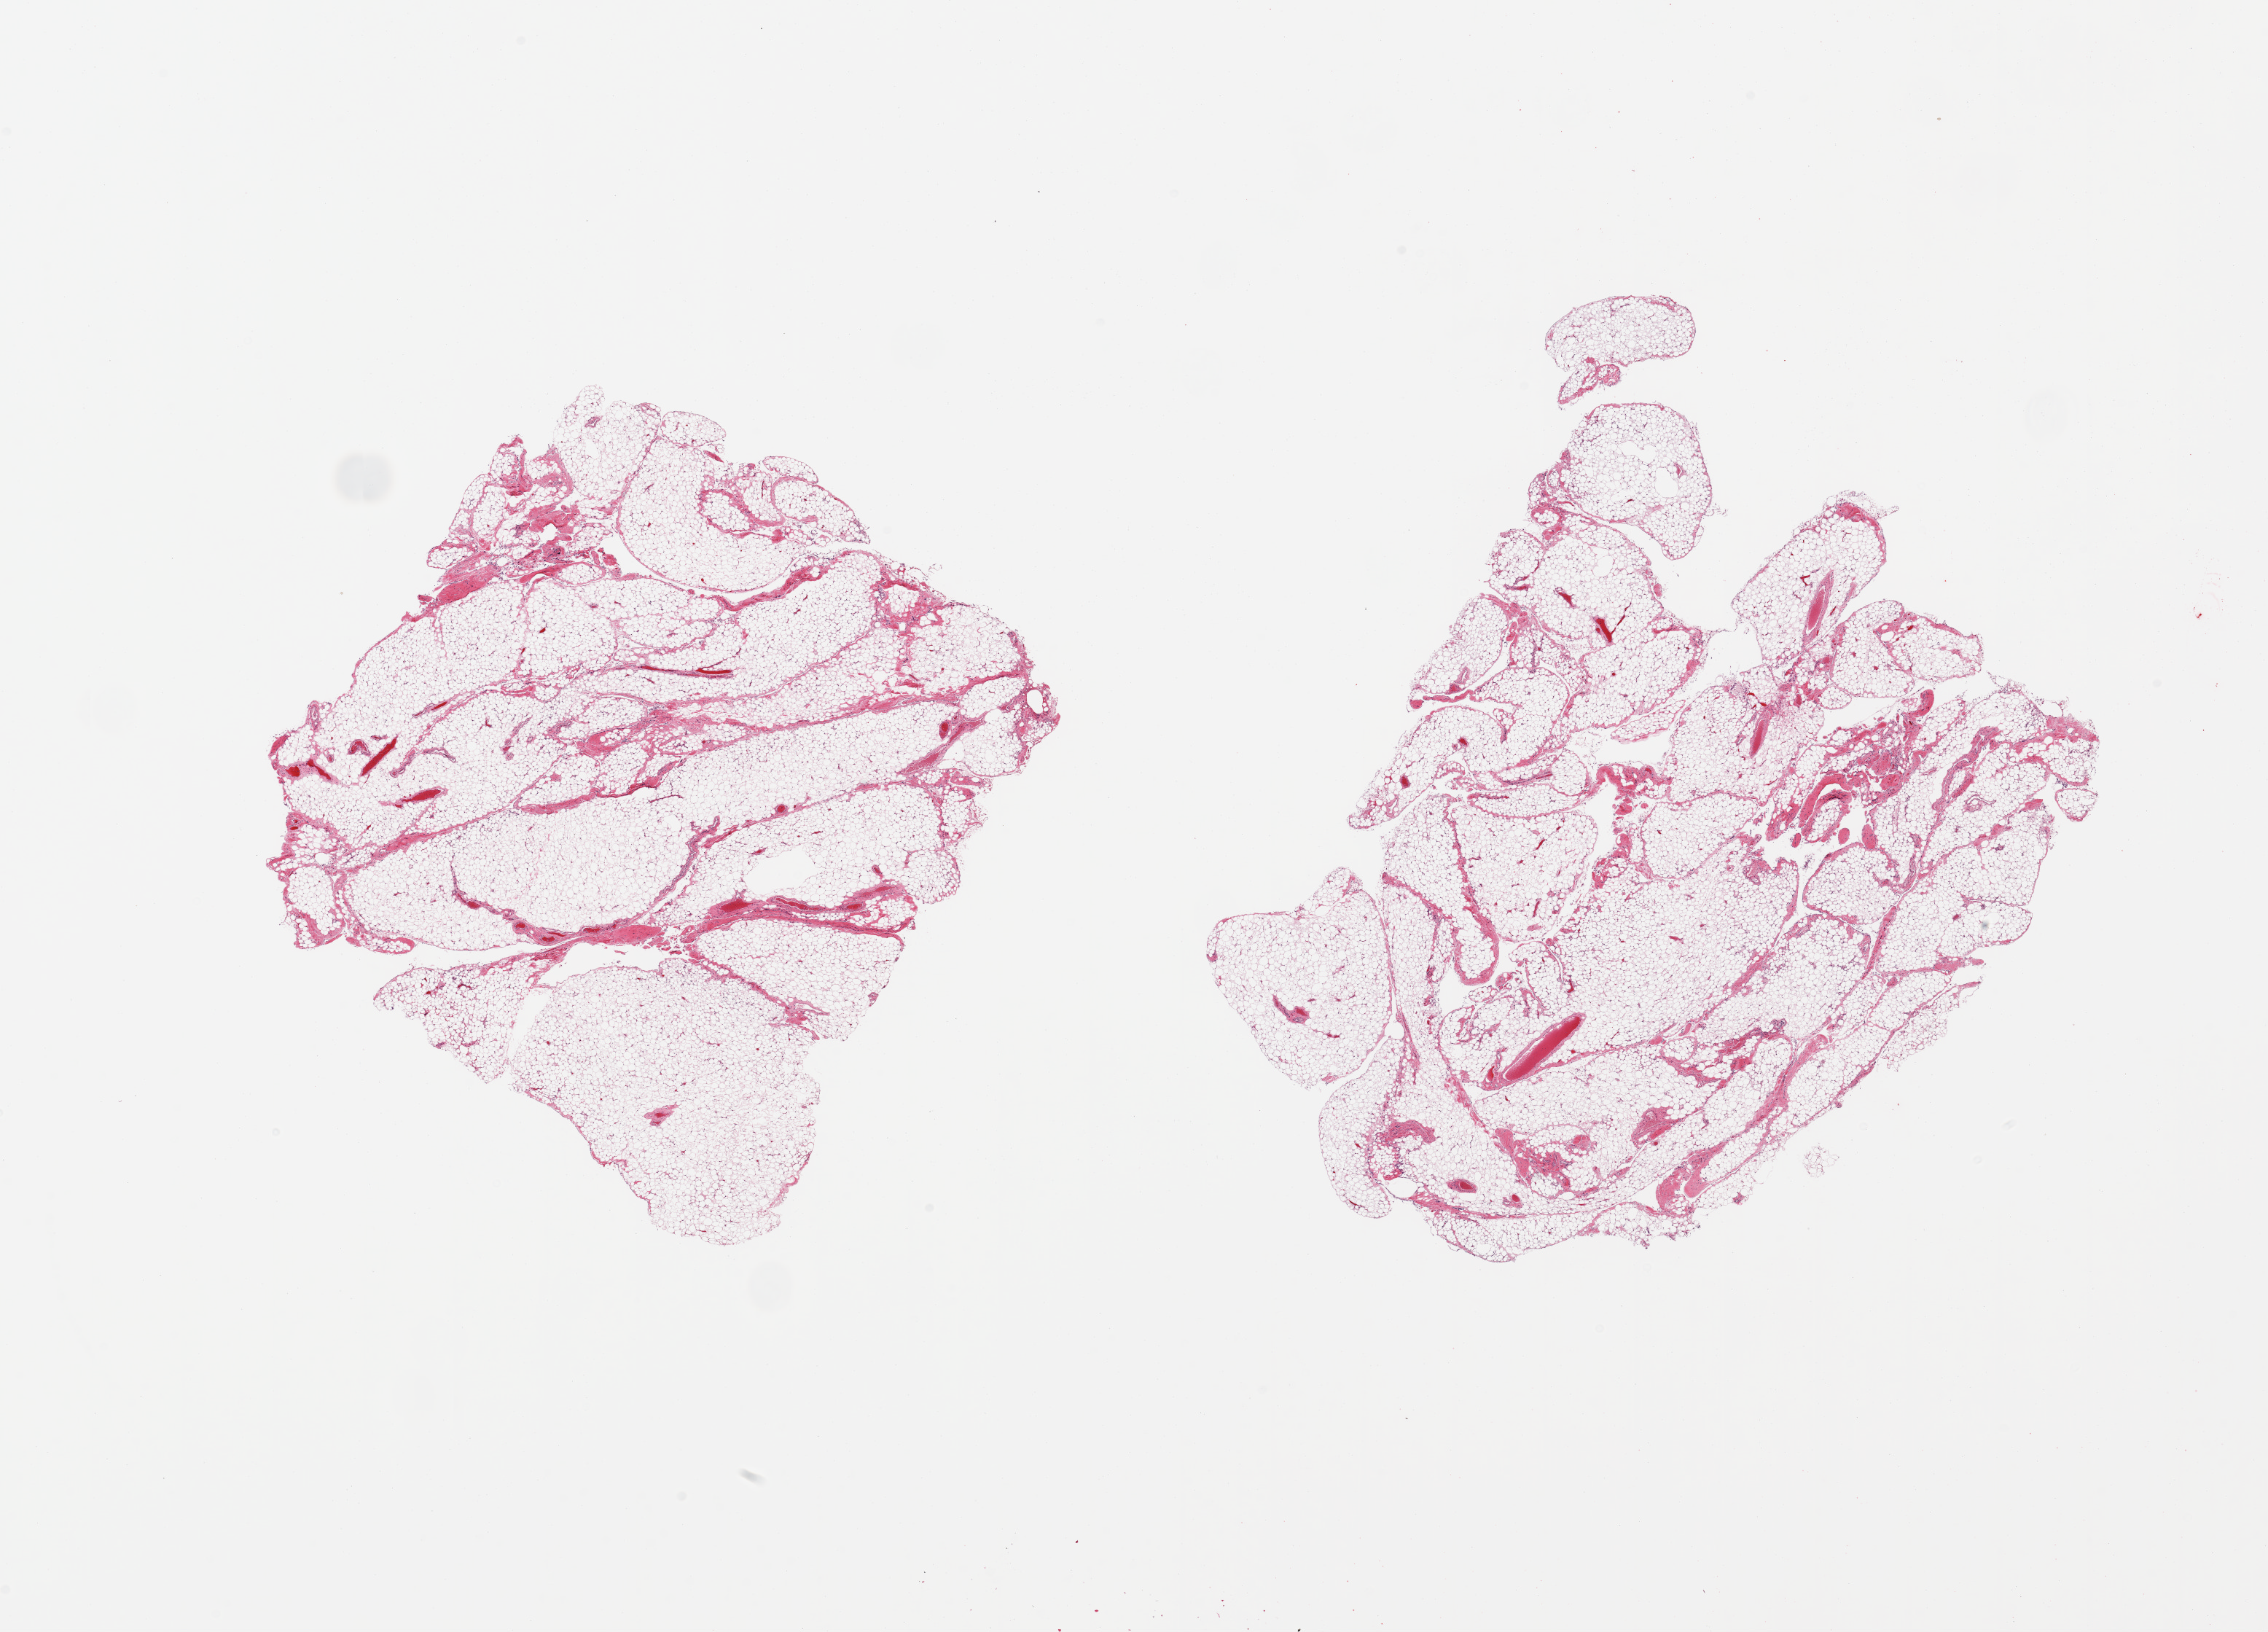
Digitized hematoxylin and eosin (H&E)-stained section, brightfield — whole scanned area (about 24.6 x 17.7 mm) shown as a low-resolution overview. PAXgene-fixed, paraffin-embedded tissue. Sampled site (target tissue): omentum. Donor tissue sample.
Reviewer comment on this tissue sample: 2 pieces, interstital fasca/vascular elements are ~20%.